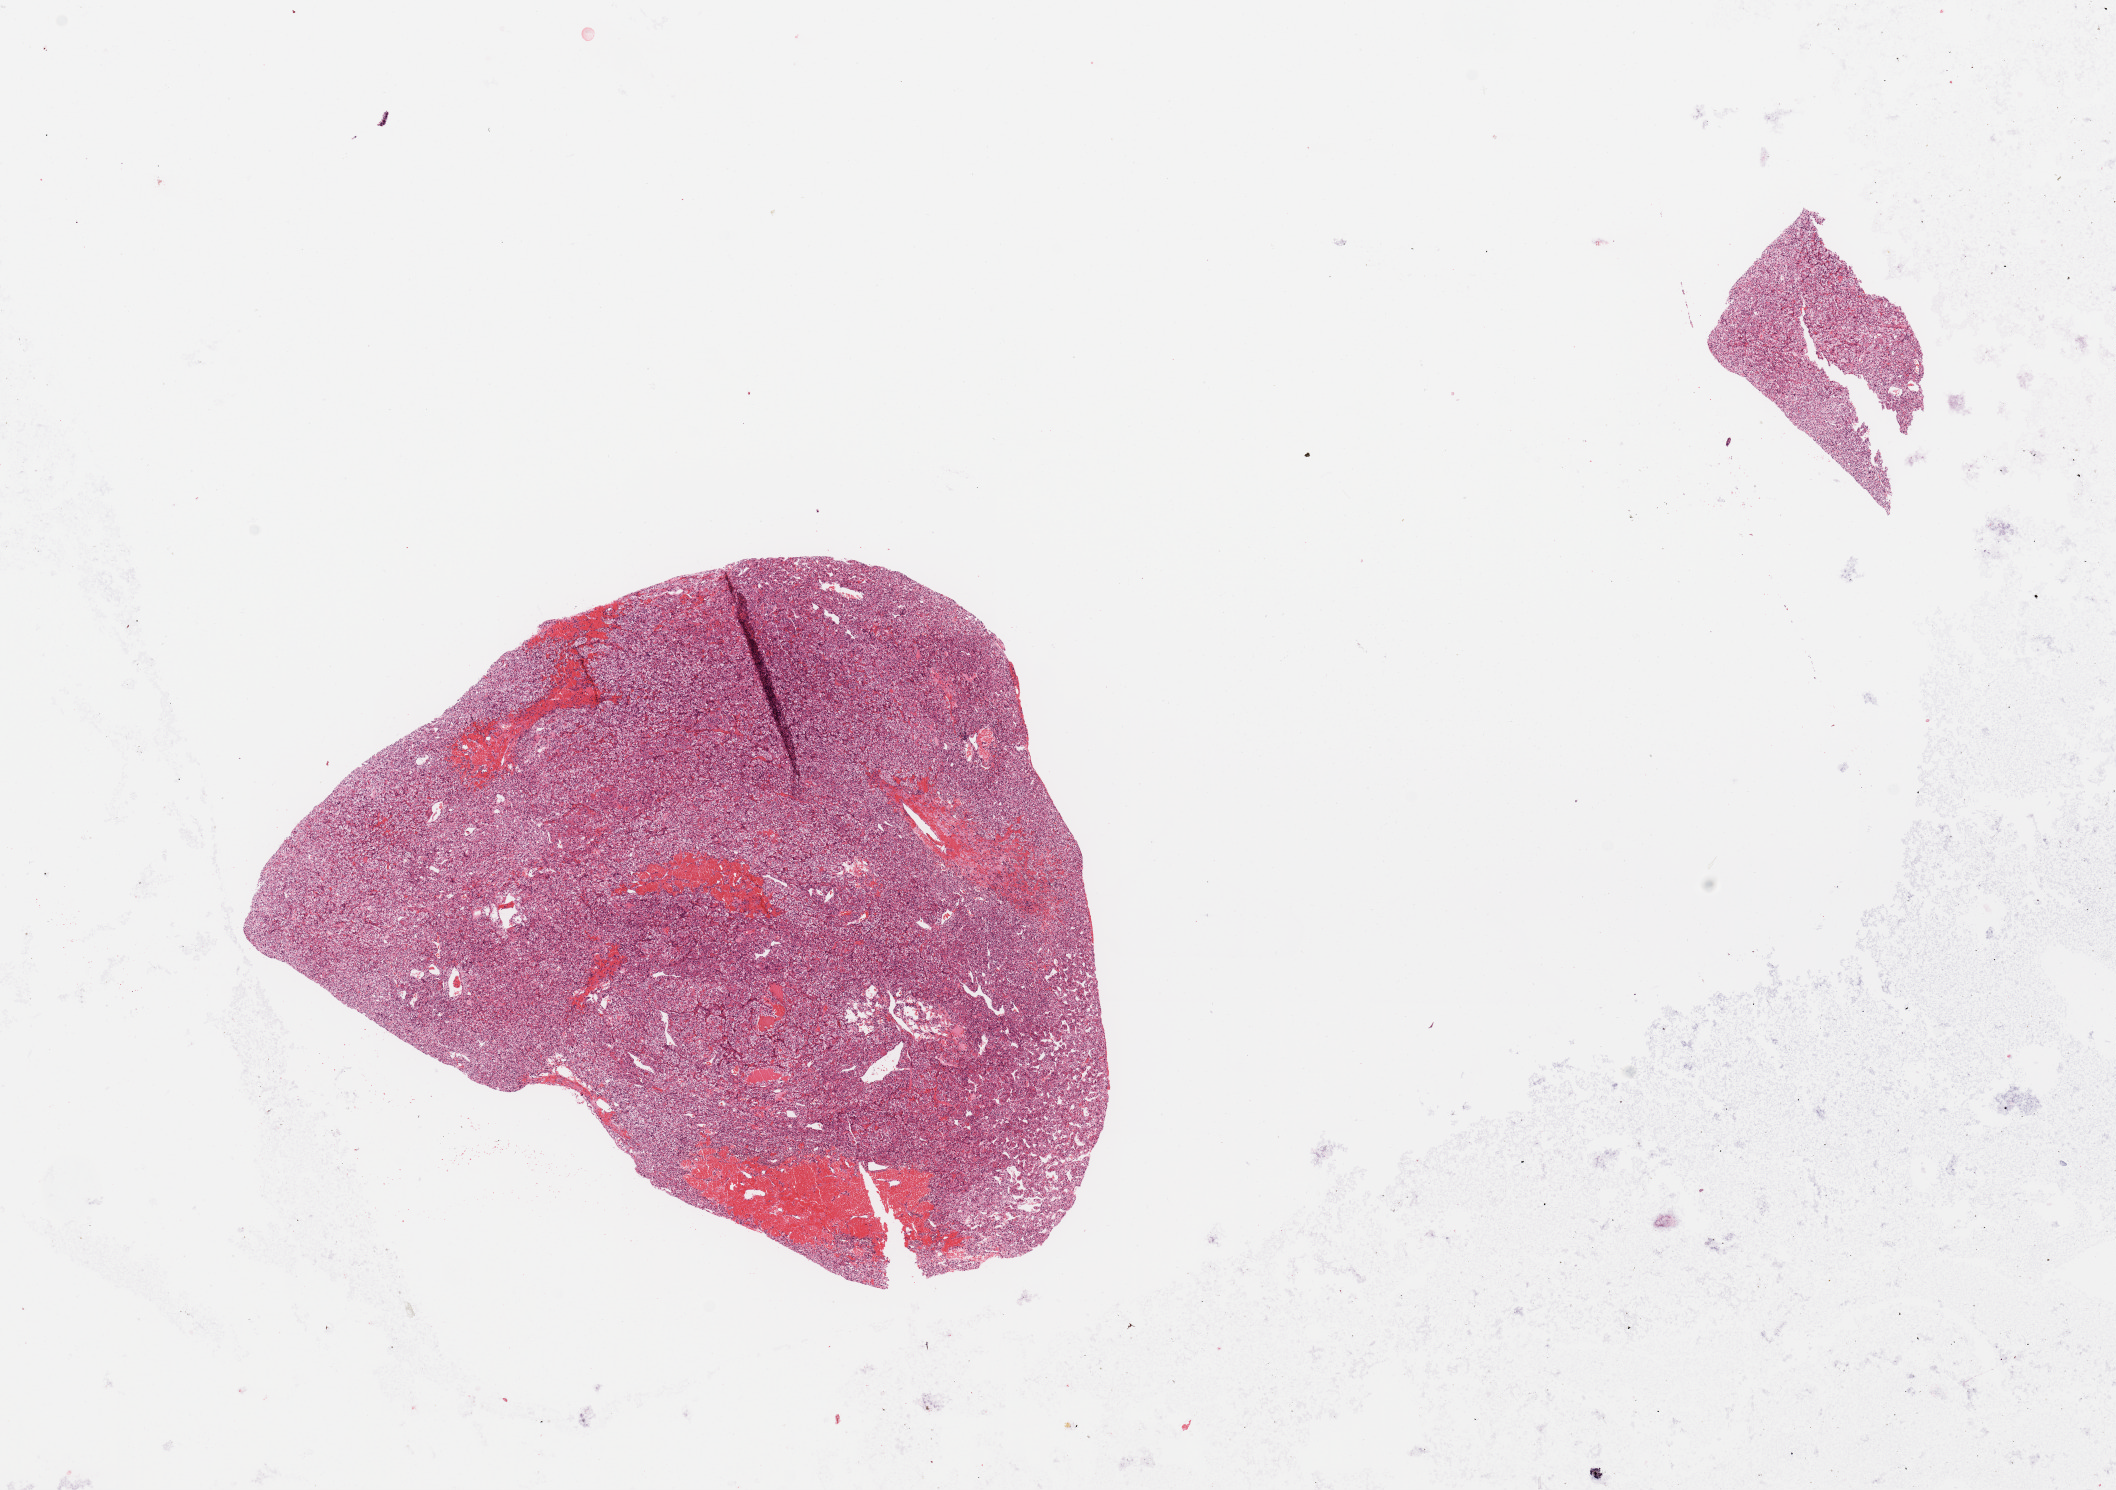
Hematoxylin and eosin (H&E) stained whole-slide image — low-resolution overview of the scanned area, about 16.7 x 11.8 mm (slide scanned at 20x), tumour tissue sample, sampled site: kidney. Male, 52 y/o. Pathologist review of this section (percent, as recorded): tumour nuclei 90%, necrosis 3%.
Diagnosis: Renal cell carcinoma, NOS.